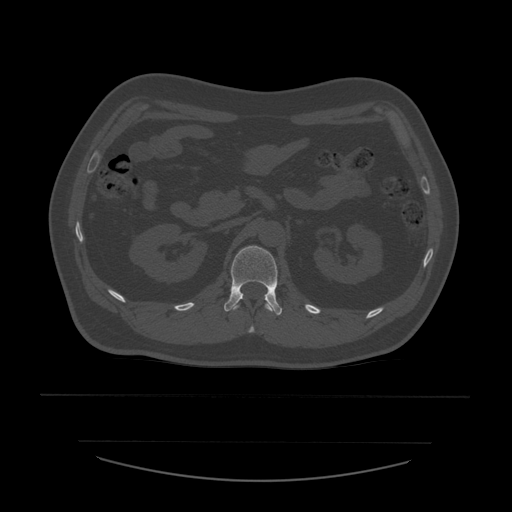
CT including the spine, one axial slice; position 233 of 532 along the scan axis; reconstruction kernel STANDARD; bone window (W 1800 / L 400 HU); 1.25 mm slice thickness; 512 × 512 image matrix, field of view 441 × 441 mm. Patient age 44 years. Case-level facts recorded for this patient, not image findings: primary cancer: soft tissue sarcoma.
Structures marked on this image (semi-automatic segmentation, software-assisted and operator-edited):
- L1 vertebra: bounding box [x1, y1, x2, y2] px = [224, 246, 283, 316]
- T12 vertebra: [234, 301, 273, 333]